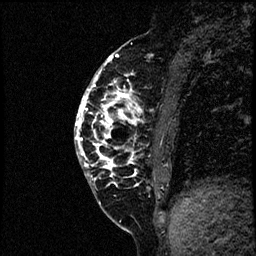
Breast MRI (dynamic contrast-enhanced), one sagittal slice. Slice 23 of 60 in the series (ordered by position). Dynamic contrast-enhanced study with each time point stored as its own series, time point 2 of 4 at this slice position (early post-contrast, ordered by acquisition time). 1.5 T. TE 4.2 ms, TR 17.6 ms. 2 mm slice thickness. 256 × 256 image matrix, field of view 200 × 200 mm. Female patient, age 40 years. From the clinical record (not read from this slice): setting: breast cancer imaged before/during neoadjuvant chemotherapy; receptor status: HER2-positive.
Outlined on this slice (semi-automatic segmentation, software-assisted and operator-edited):
- analysis volume of interest (the breast-tissue region the enhancement analysis was run in; not a lesion): bounding box [x1, y1, x2, y2] px = [76, 56, 197, 205]
- tumour enhancement mask (voxels above the 100 % enhancement threshold inside the analysis volume of interest): [76, 56, 142, 181]